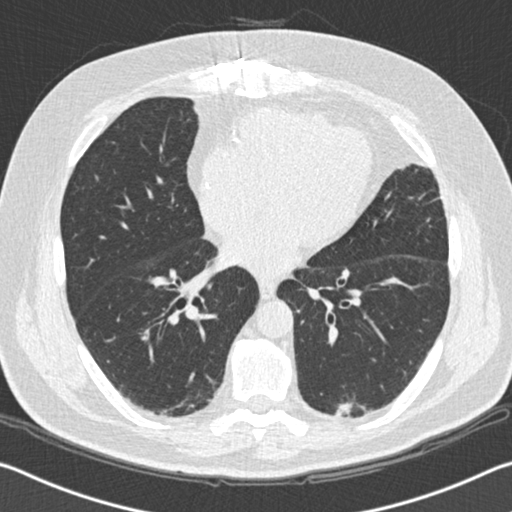
Chest CT (low-dose screening protocol), one axial image, second screening round (one year after baseline), lung window (W 1500 / L -600 HU), 2 mm slice thickness. Male participant, aged 65 years at enrolment. Former smoker at enrolment.
- Expert reader's lesion annotation, bounding box [x1, y1, x2, y2] px = [324, 387, 383, 435].
- The exam's reader record, not a measurement of the box and not confirmed to be the same lesion: non-calcified nodule or mass ≥4 mm, left lower lobe, 19 × 11 mm, spiculated (stellate) margins, soft tissue attenuation, pre-existing on the prior screen: yes; interval growth: yes.
- Official screen result: positive, change unspecified: nodule(s) >= 4 mm or enlarging nodule(s), mass(es), or other non-specific abnormalities suspicious for lung cancer.
- Participant outcome: lung cancer diagnosed 179 days after this screen — squamous cell carcinoma, NOS, left lower lobe, moderately differentiated (G2), stage IA (AJCC 6th edition), 20 mm at pathology.